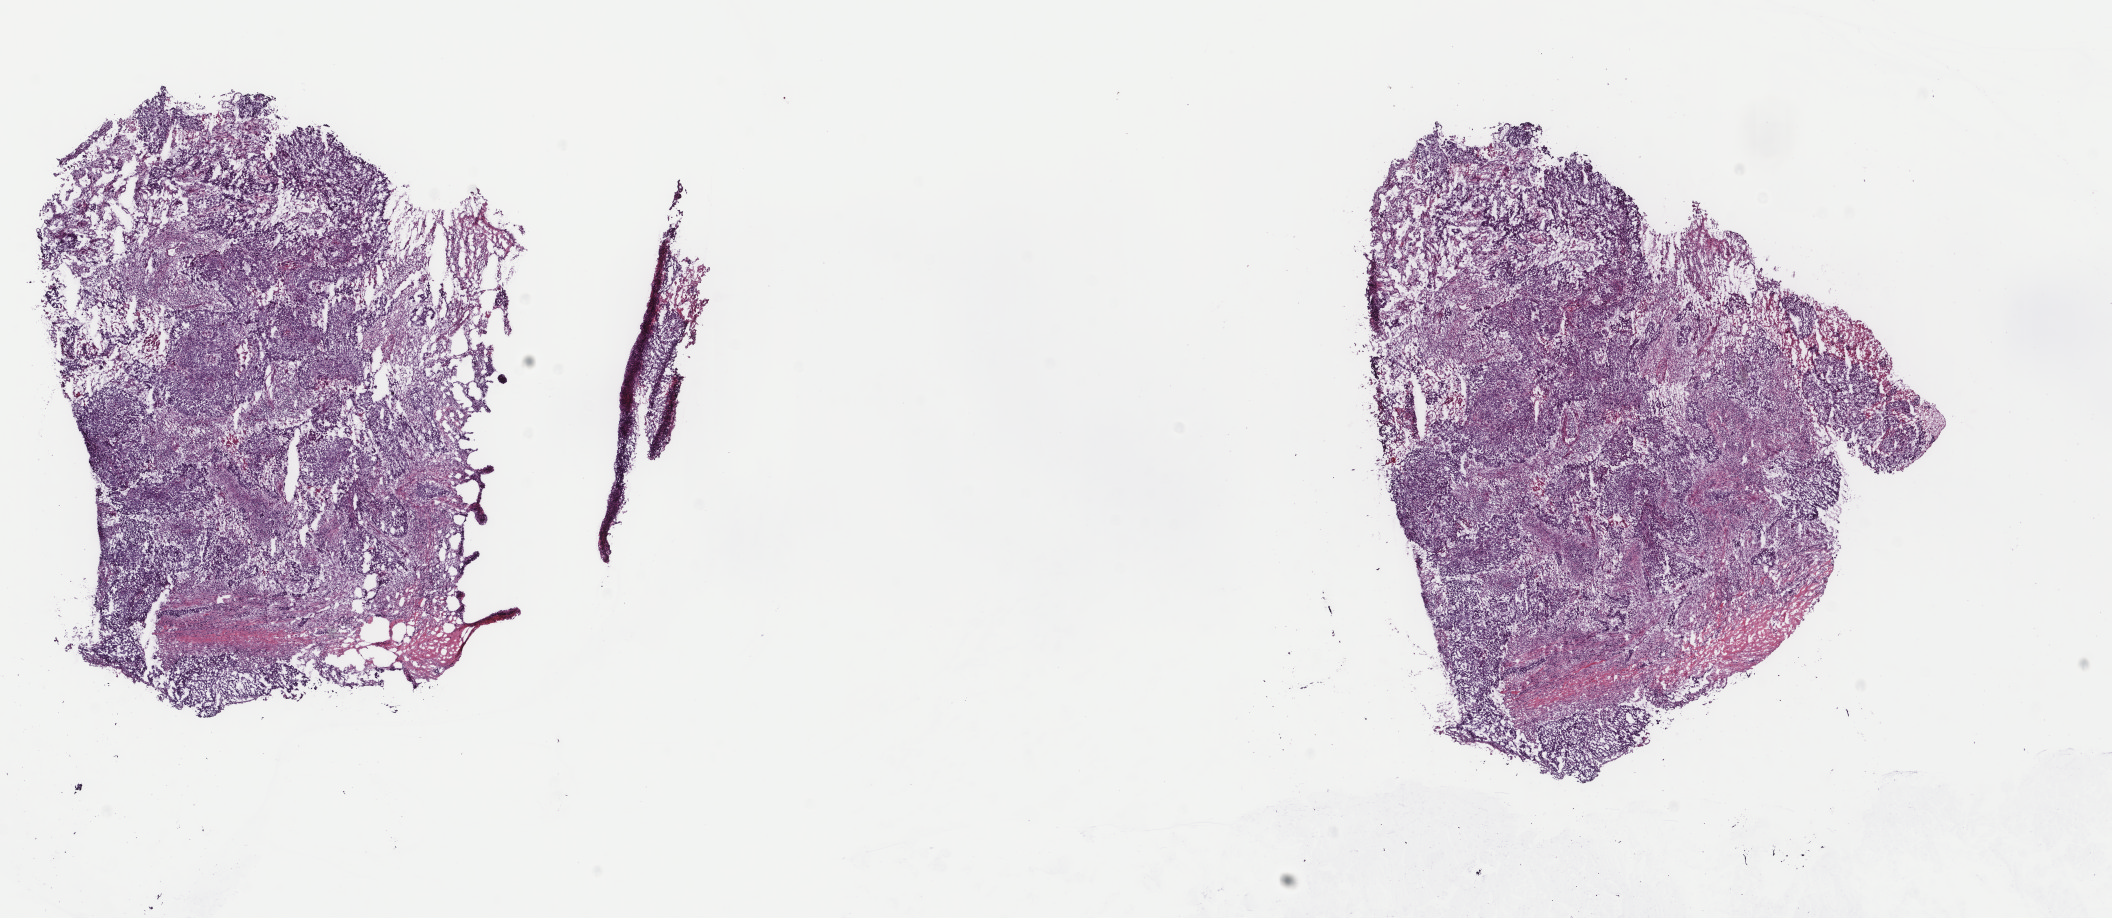
Whole-slide histology image, H&E-stained — whole scanned area (about 16.8 x 7.3 mm, from a 40x scan) shown as a low-resolution overview, frozen section from the top of the tissue portion, lung, primary tumour sample. Male patient; age at initial diagnosis 54 years. Composition of this section per pathologist review: tumour cells 70%, tumour nuclei 80%, normal cells 0%, stromal cells 30%, necrosis 0%. Infiltration values recorded for this section: lymphocyte infiltration 0%, monocyte infiltration 0%, neutrophil infiltration 0%.
• histologic diagnosis: Squamous cell carcinoma, NOS
• AJCC pathologic stage: IIB (6th edition)